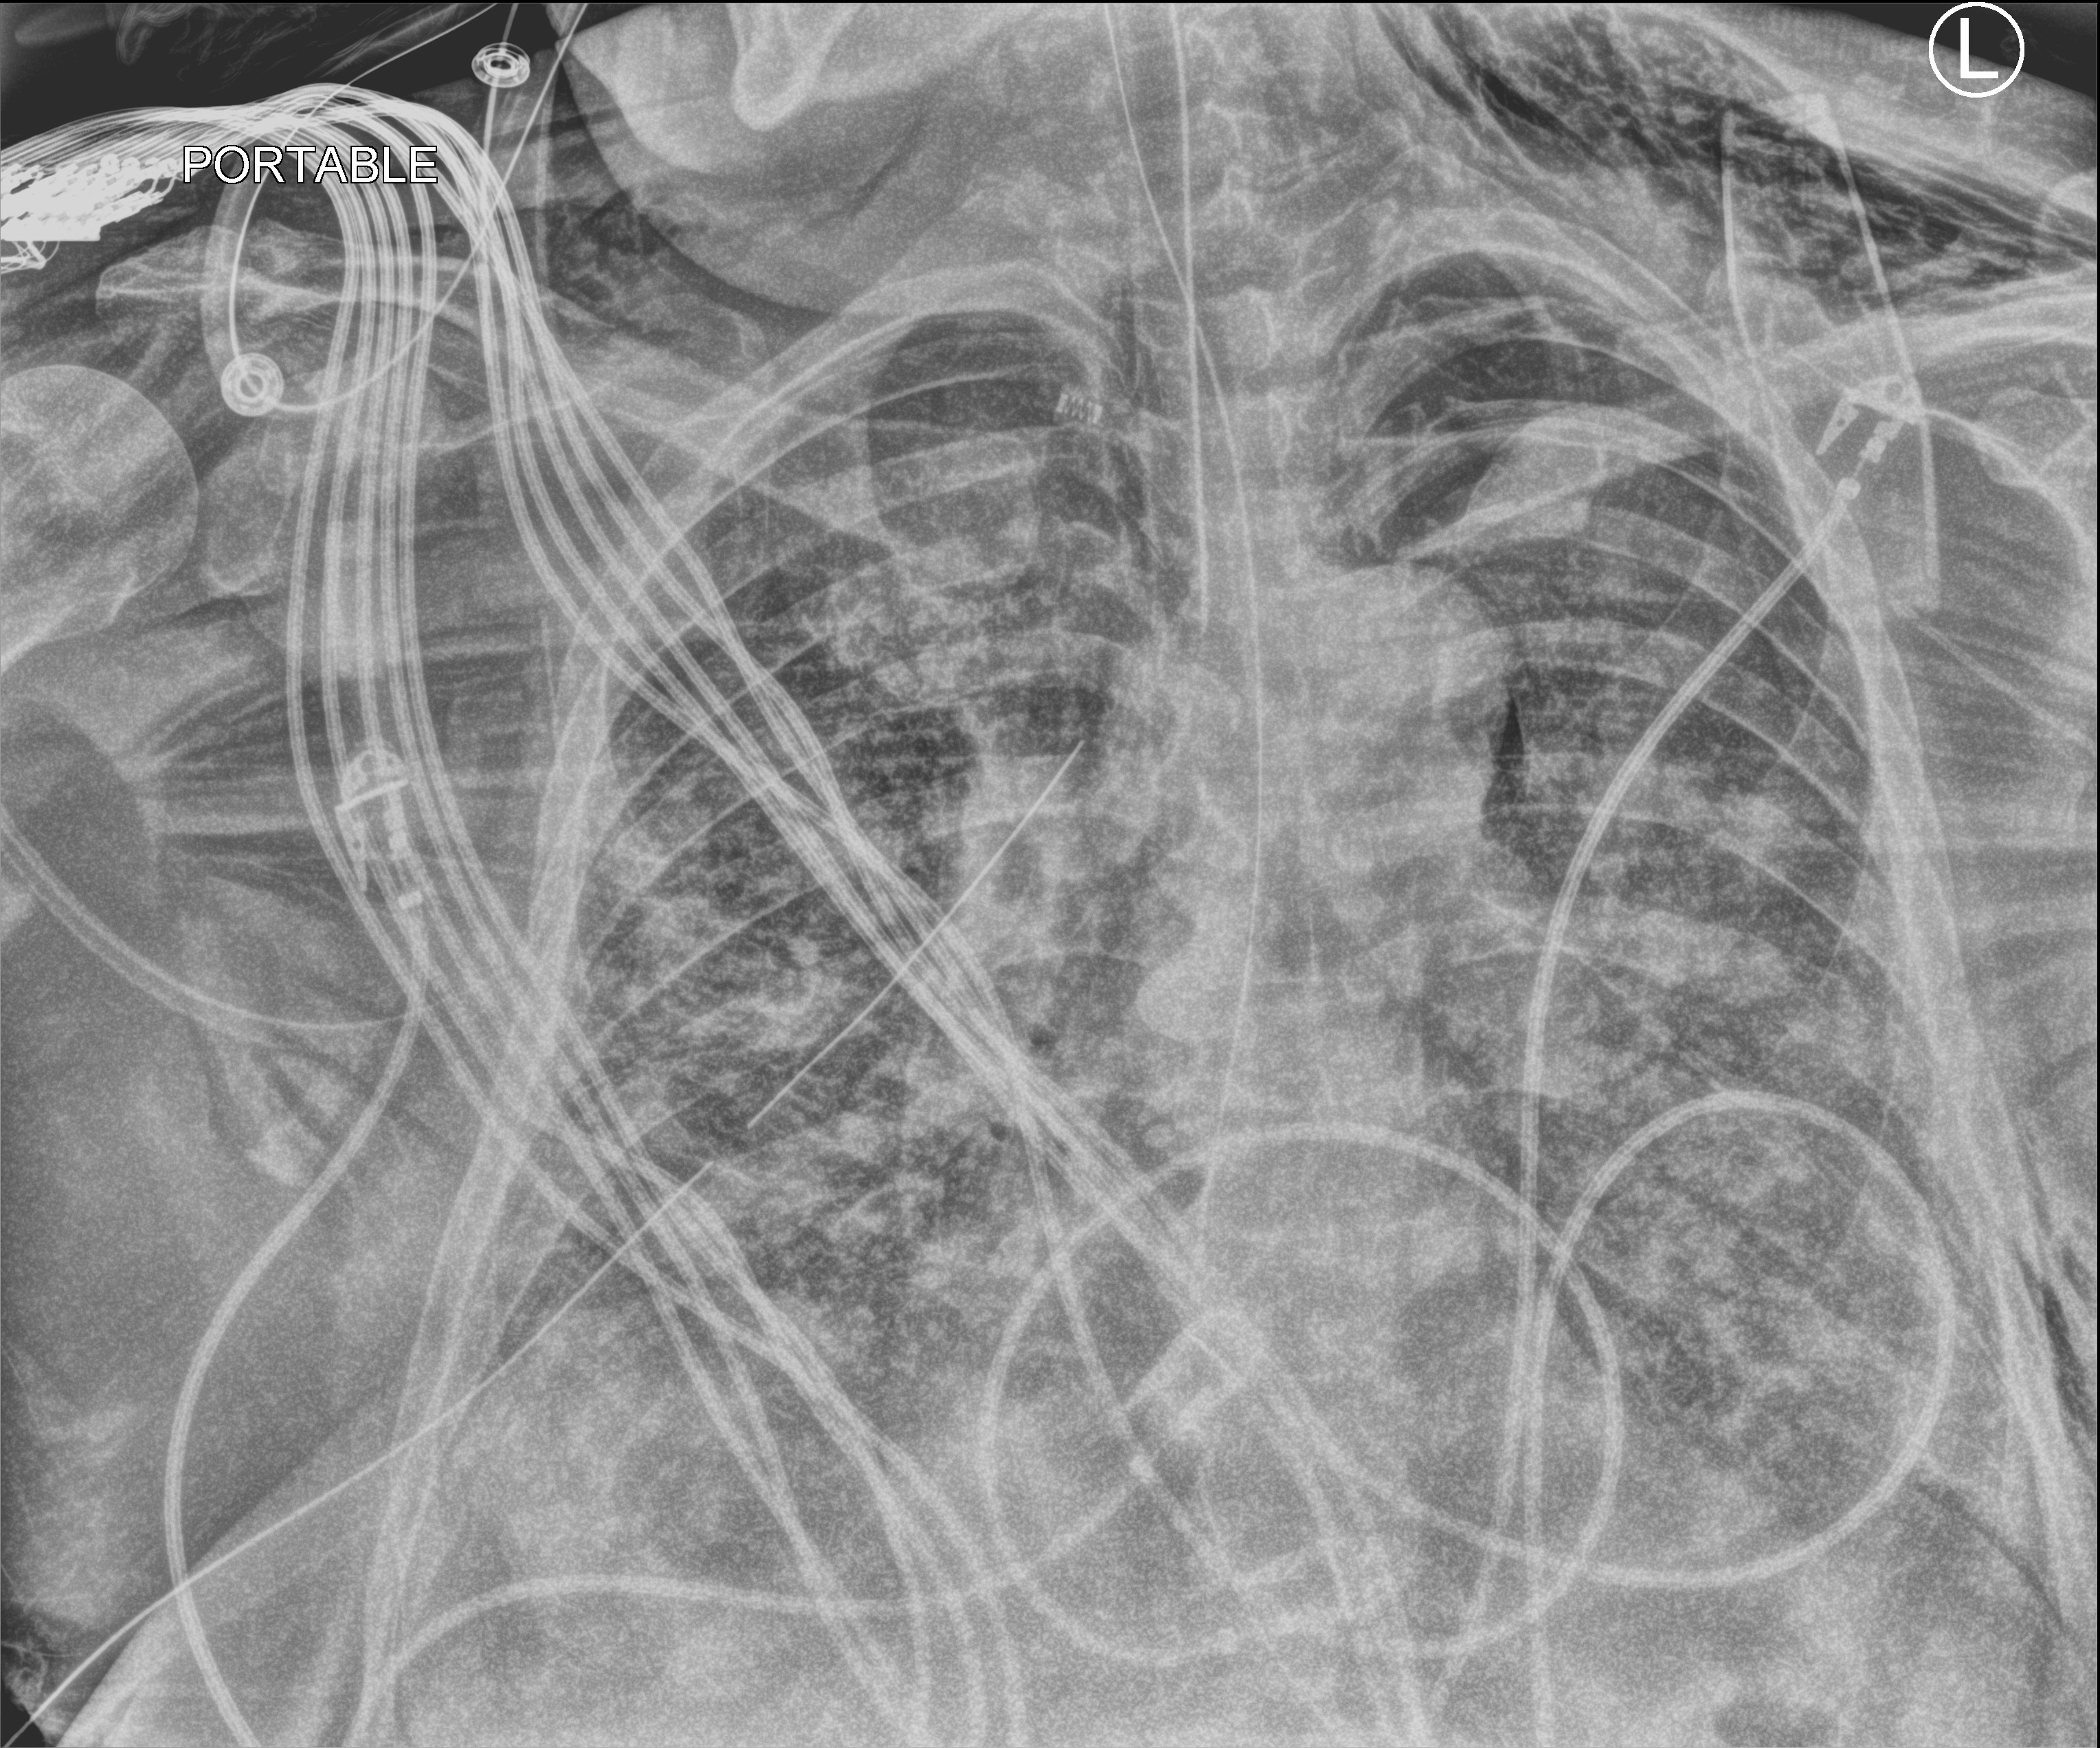
Chest X-ray (portable), anteroposterior (AP) projection. Patient hospitalised with COVID-19, aged 18–59 years.
From the hospital-stay record, not from the radiograph (when in the stay this image was taken is not recorded): admitted to intensive care during this hospital stay: yes.